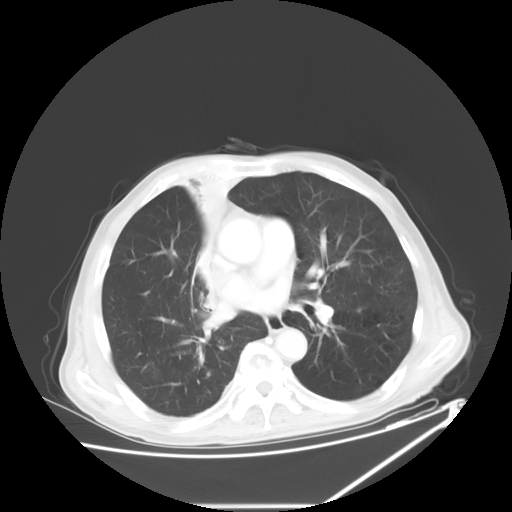
Chest CT, one axial slice. Position 33 of 60 along the scan axis. Reconstruction kernel STANDARD. 120 kVp. Lung window (W 1500 / L -600 HU). 5 mm slice thickness. 512 × 512 image matrix. Patient: male, 73 years. From the clinical record (not read from this slice): clinical TNM (as recorded): T2a N1 M0.
Outlined on this slice (bounding box drawn by a radiologist):
- lung tumour (recorded histology: squamous cell carcinoma): bounding box (x1, y1, x2, y2) in pixels: (184, 180, 237, 328)